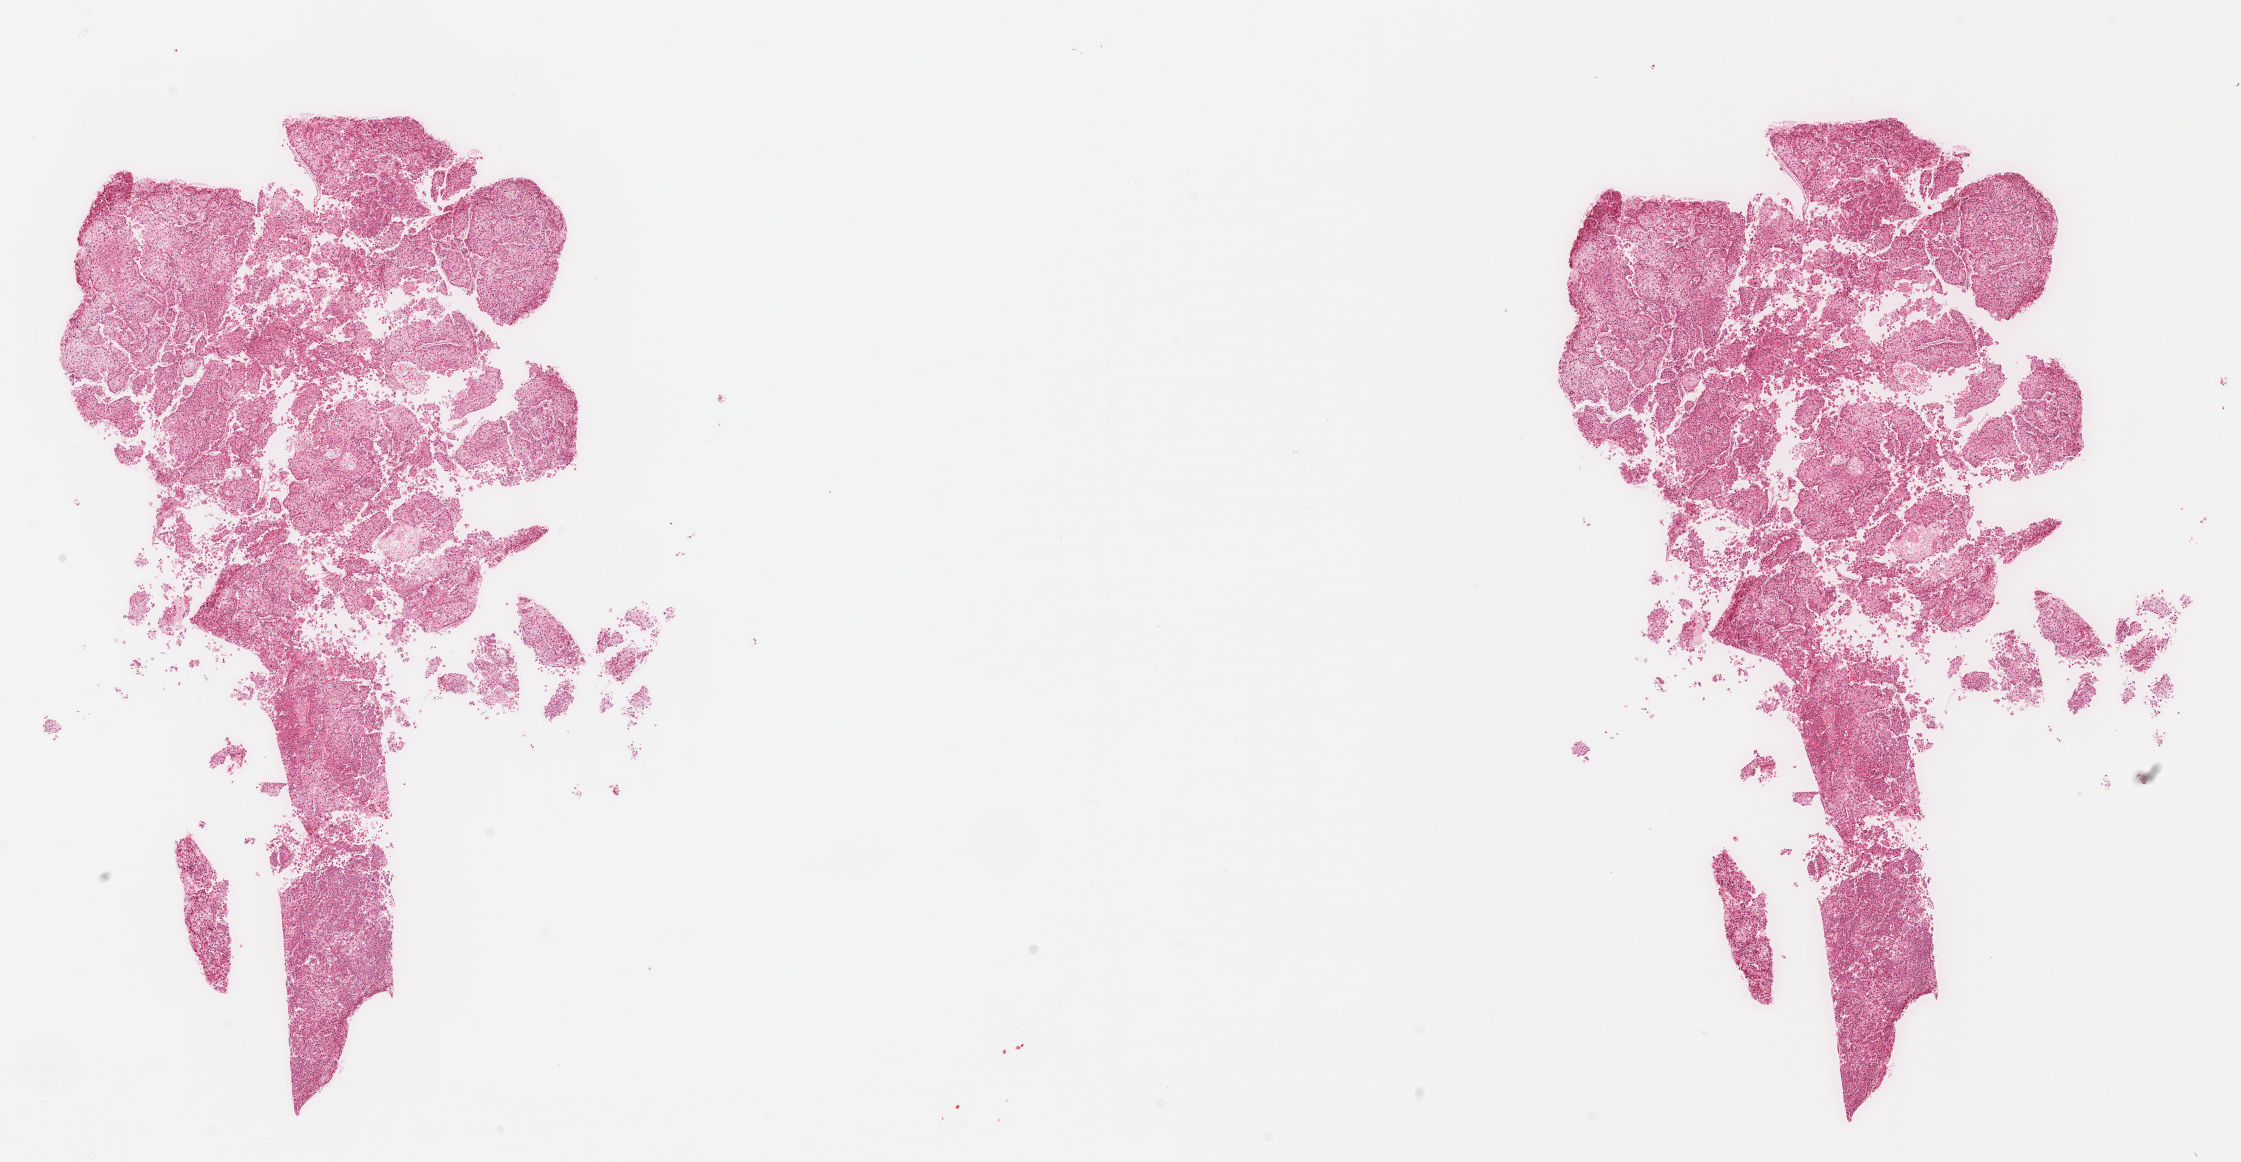
Whole-slide histology image, H&E — whole scanned area (about 18.1 x 9.4 mm) shown as a low-resolution overview; formalin-fixed paraffin-embedded (FFPE) diagnostic section; primary tumour sample from the liver. Patient: male, age at initial diagnosis 58 years.
Diagnosis: Hepatocellular carcinoma, NOS.